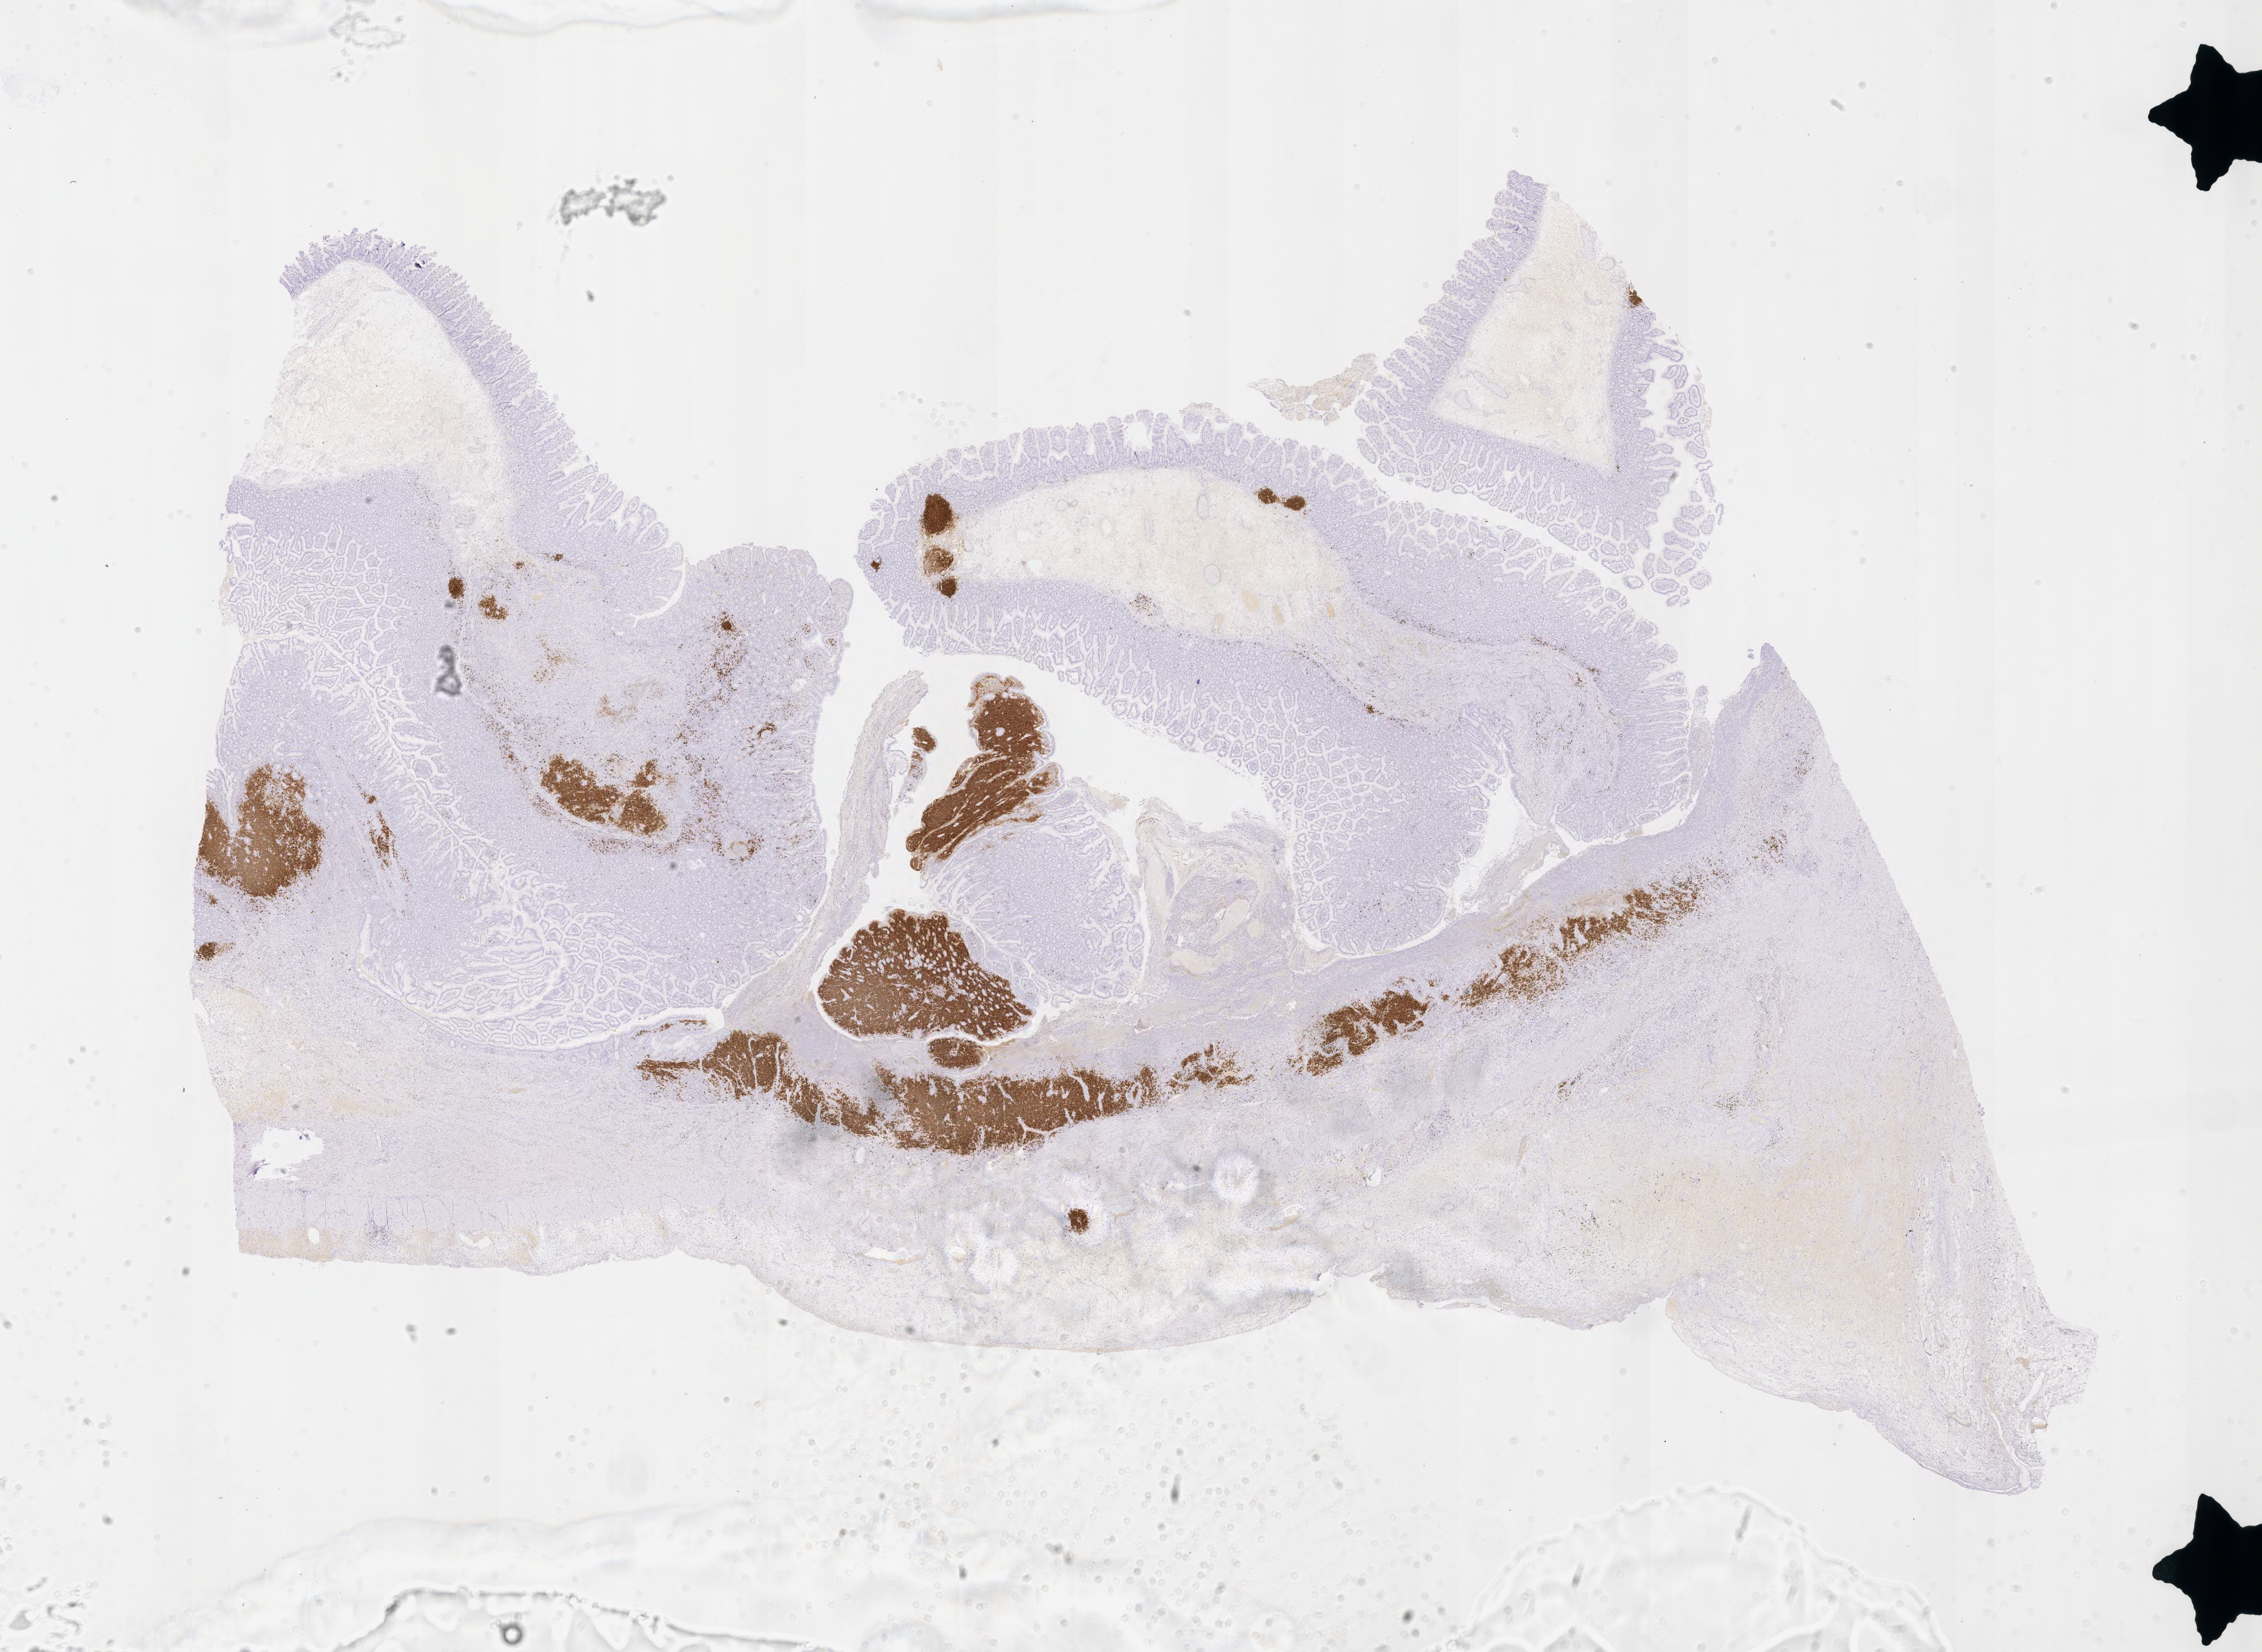
Immunohistochemistry (IHC) whole-slide image stained for CD20, a low-resolution overview of the entire scanned area, about 29.7 x 21.7 mm, specimen: tumor tissue. Female patient, 44 years old.
* histologic diagnosis: Burkitt lymphoma, NOS